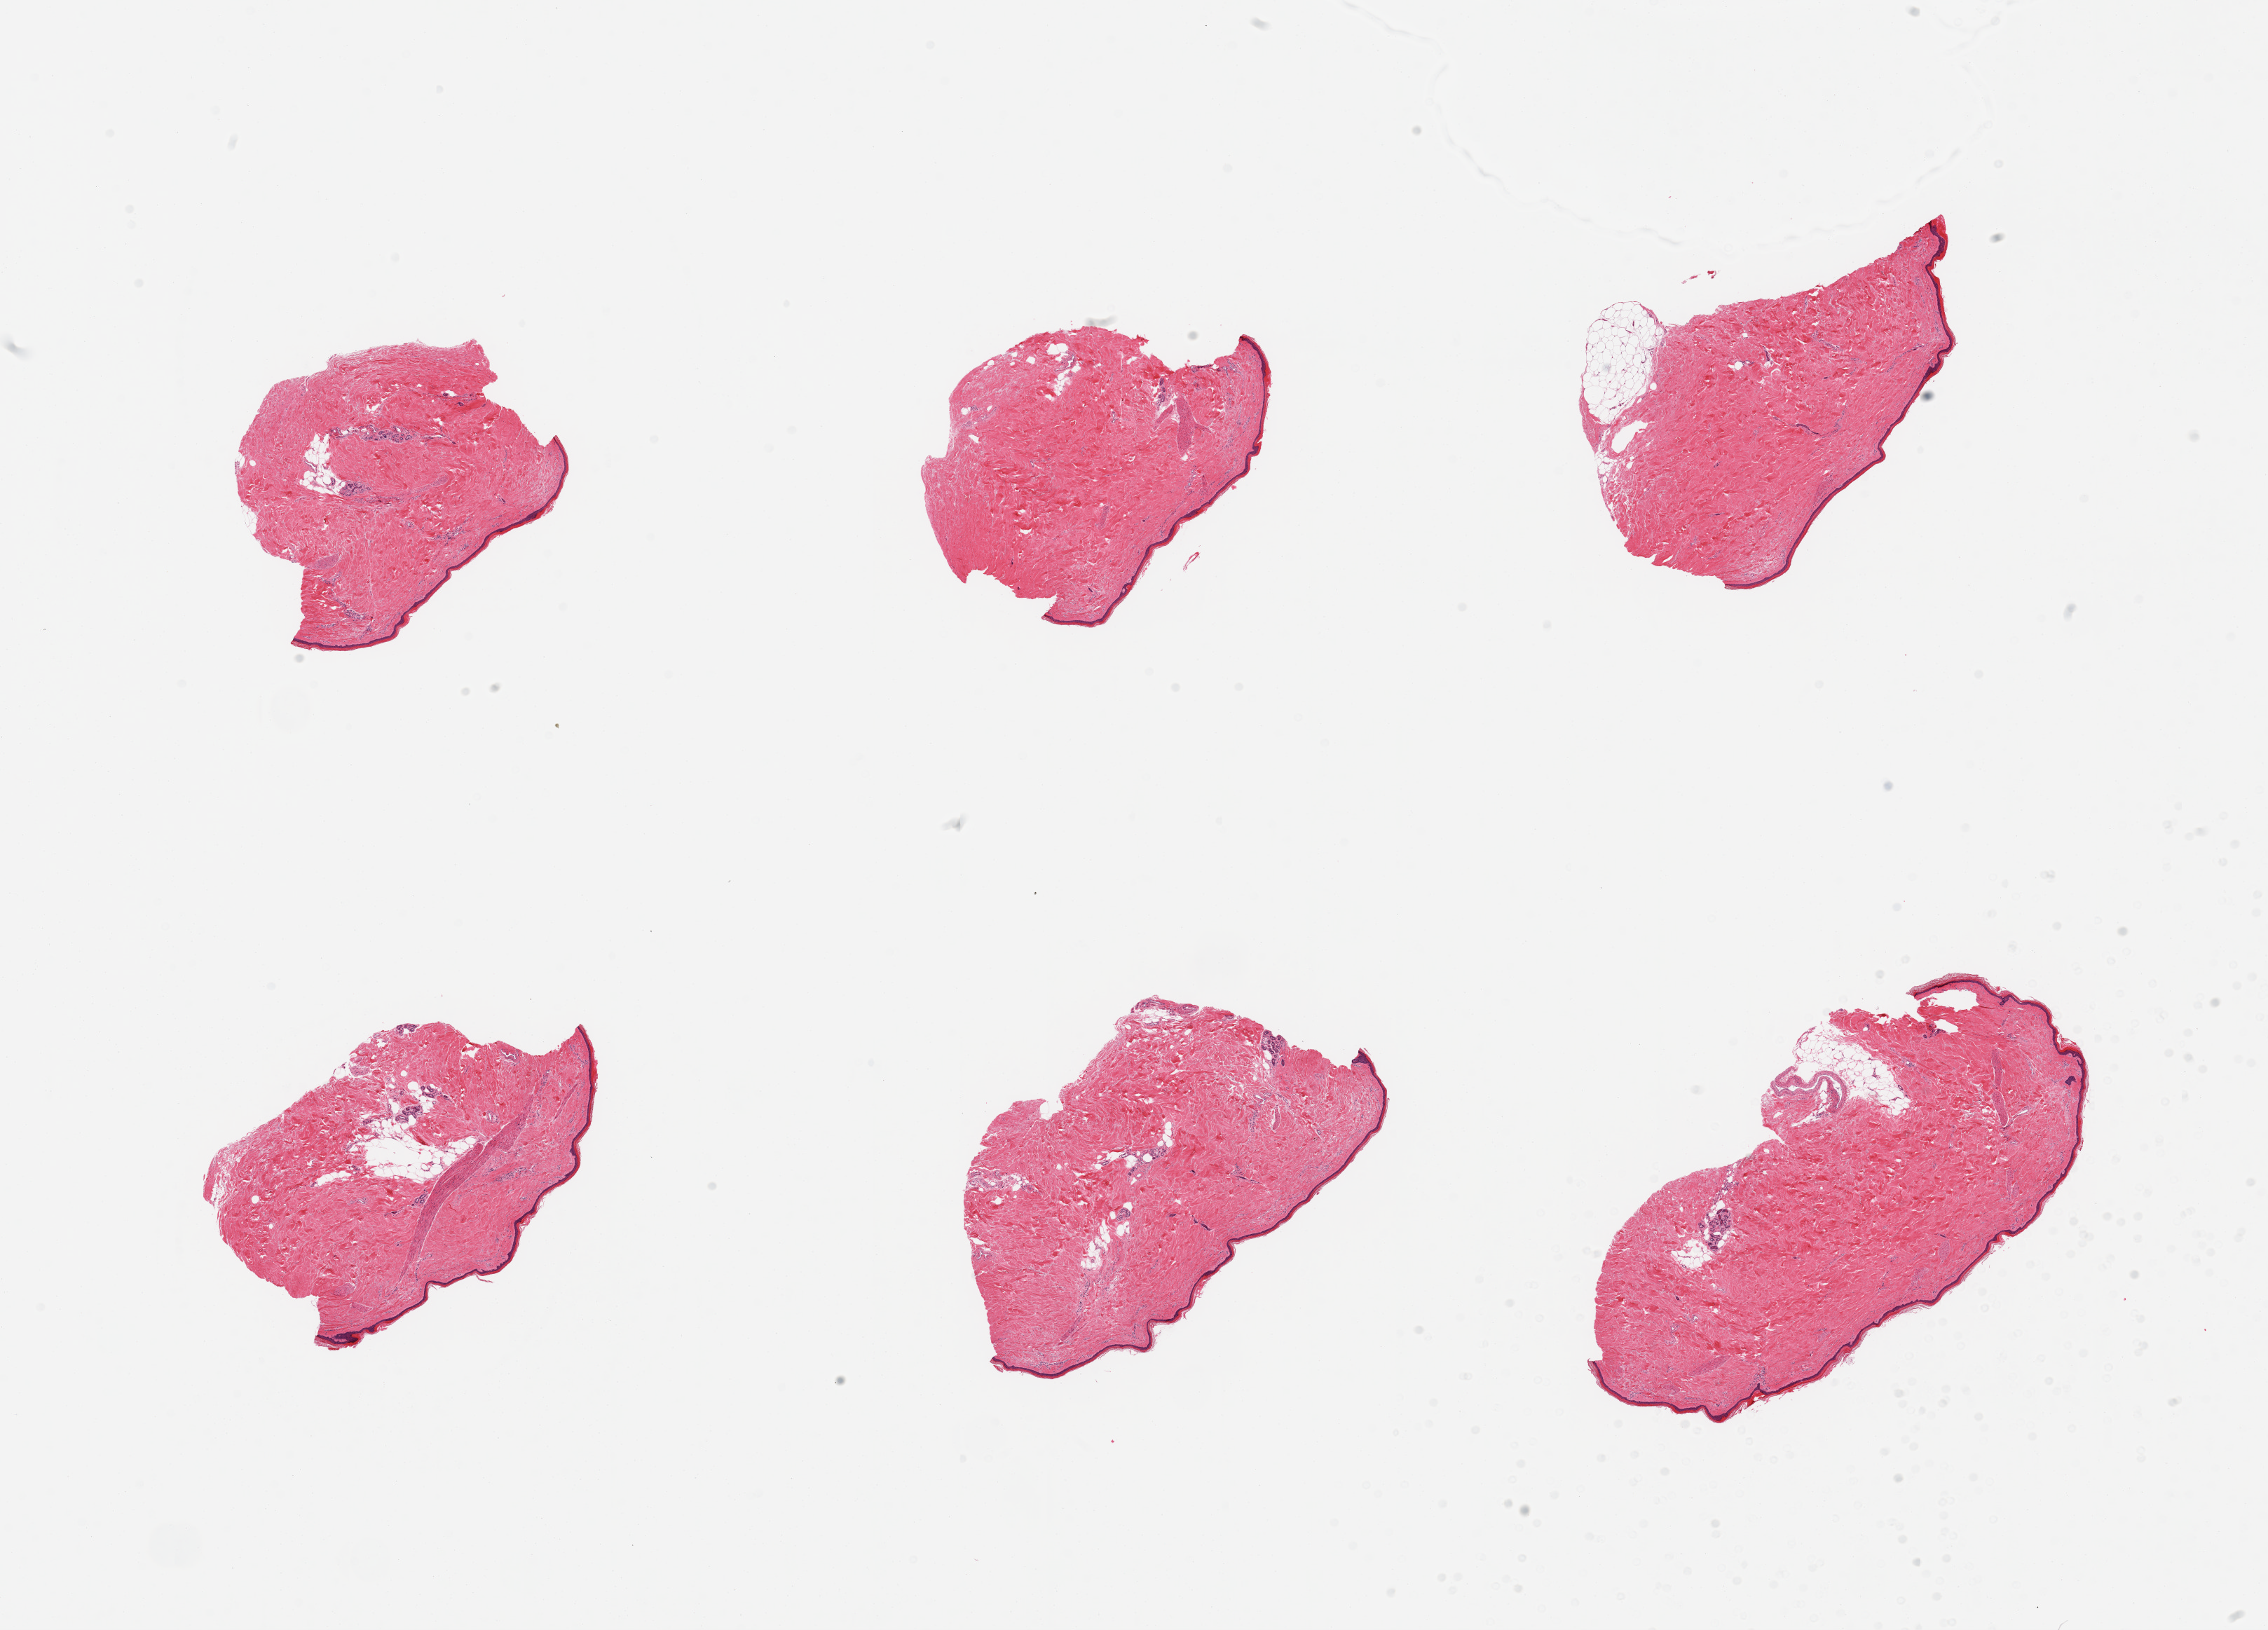
Hematoxylin and eosin (H&E) whole-slide image, brightfield, a low-resolution overview of the entire scanned area, about 25.6 x 18.4 mm; PAXgene-fixed paraffin-embedded (PFPE) section; section of skin of lower leg (target tissue); tissue donor sample.
* review note (as recorded): 6 pieces, no dermal fat; squamous epithelium is ~50 Microns